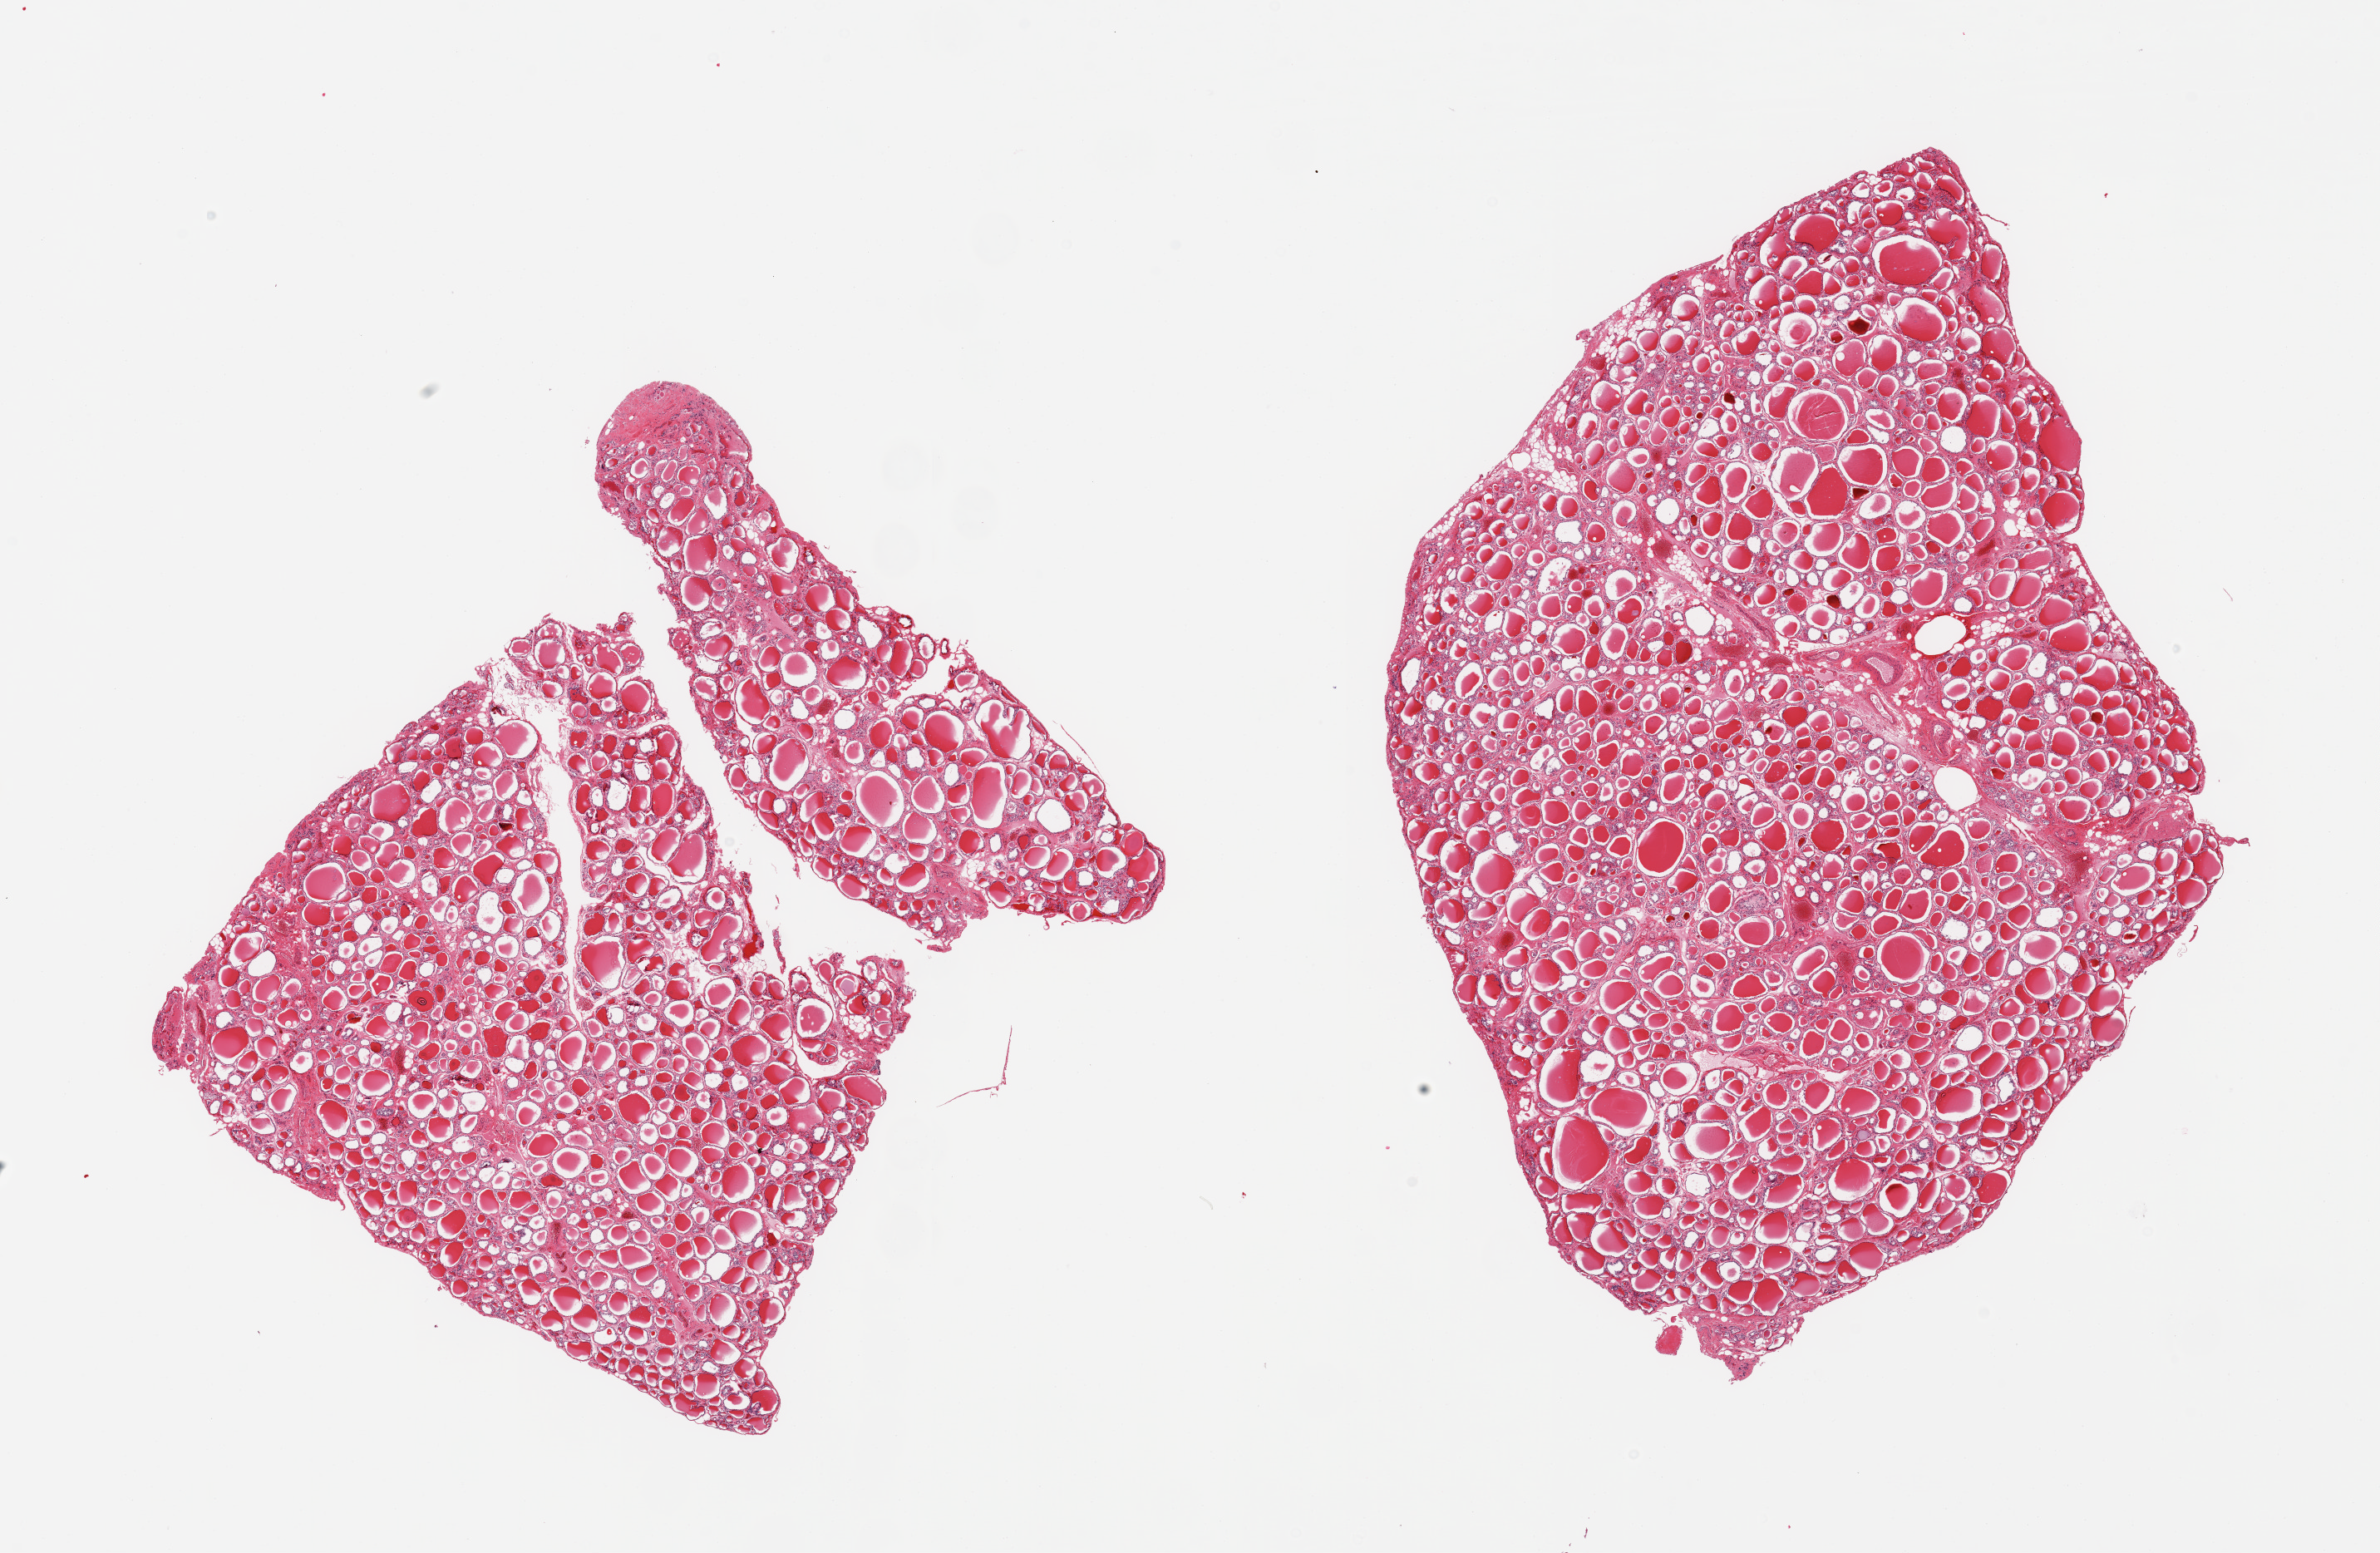
Digitized H&E-stained section — low-resolution overview of the scanned area, about 22.6 x 14.8 mm. PAXgene-fixed, paraffin-embedded tissue. Target tissue: thyroid. Tissue donor sample. Donor: male.
Review note (as recorded): 2 pieces; well trimmed.